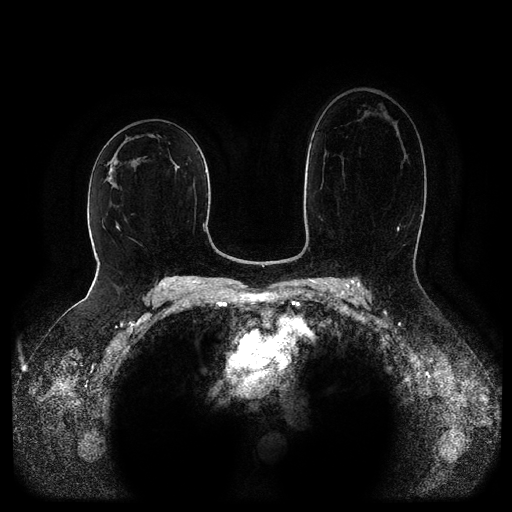
Breast MRI (dynamic contrast-enhanced, multi-phase), one axial slice. Position 57 of 116 along the scan axis. Dynamic contrast-enhanced series, time point 2 of 5 at this slice position (early post-contrast). 1.5 T. TE 2.6 ms, TR 5.2 ms. 512 × 512 image matrix, field of view 380 × 380 mm. Female patient, age 52 years.
Annotated regions visible in this slice (semi-automatically segmented with operator editing):
- breast lesion (labelled 'tumour' in the annotation; benign lesions carry a separate 'benign' label): bounding box <170,159,180,172> (left, top, right, bottom; pixels)